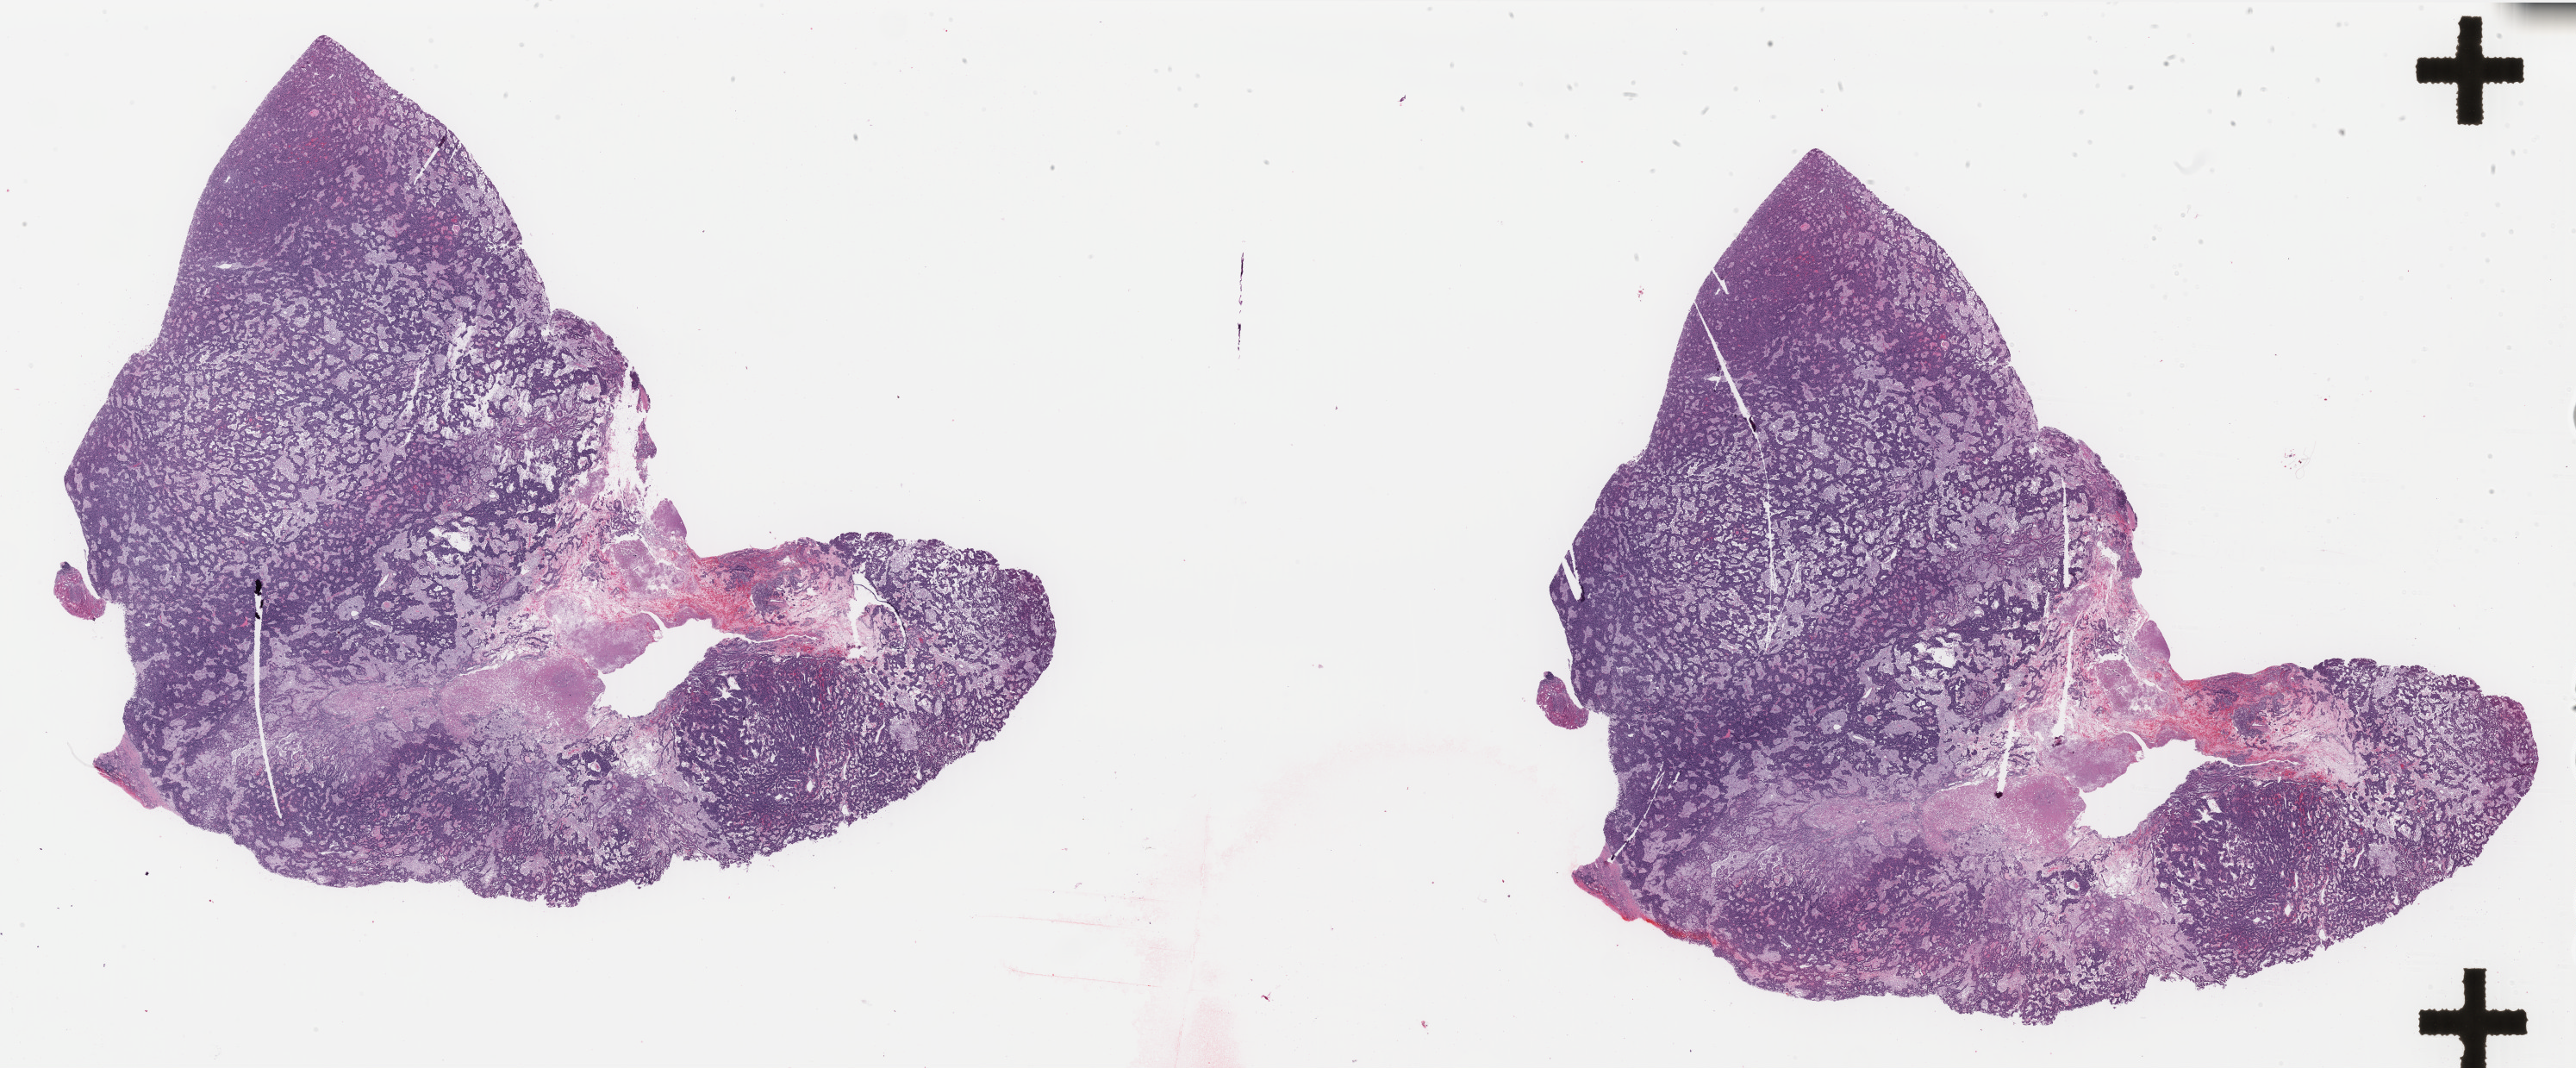
H&E-stained whole-slide image, whole scanned area (about 47.3 x 19.6 mm, from a 40x scan) shown as a low-resolution overview. Formalin-fixed paraffin-embedded (FFPE) diagnostic section. Kidney, primary tumour sample. Patient: male, age at initial diagnosis 52 years.
Diagnosis: Papillary adenocarcinoma, NOS. Laterality: right. TNM: T1a NX MX. AJCC pathologic stage: I.